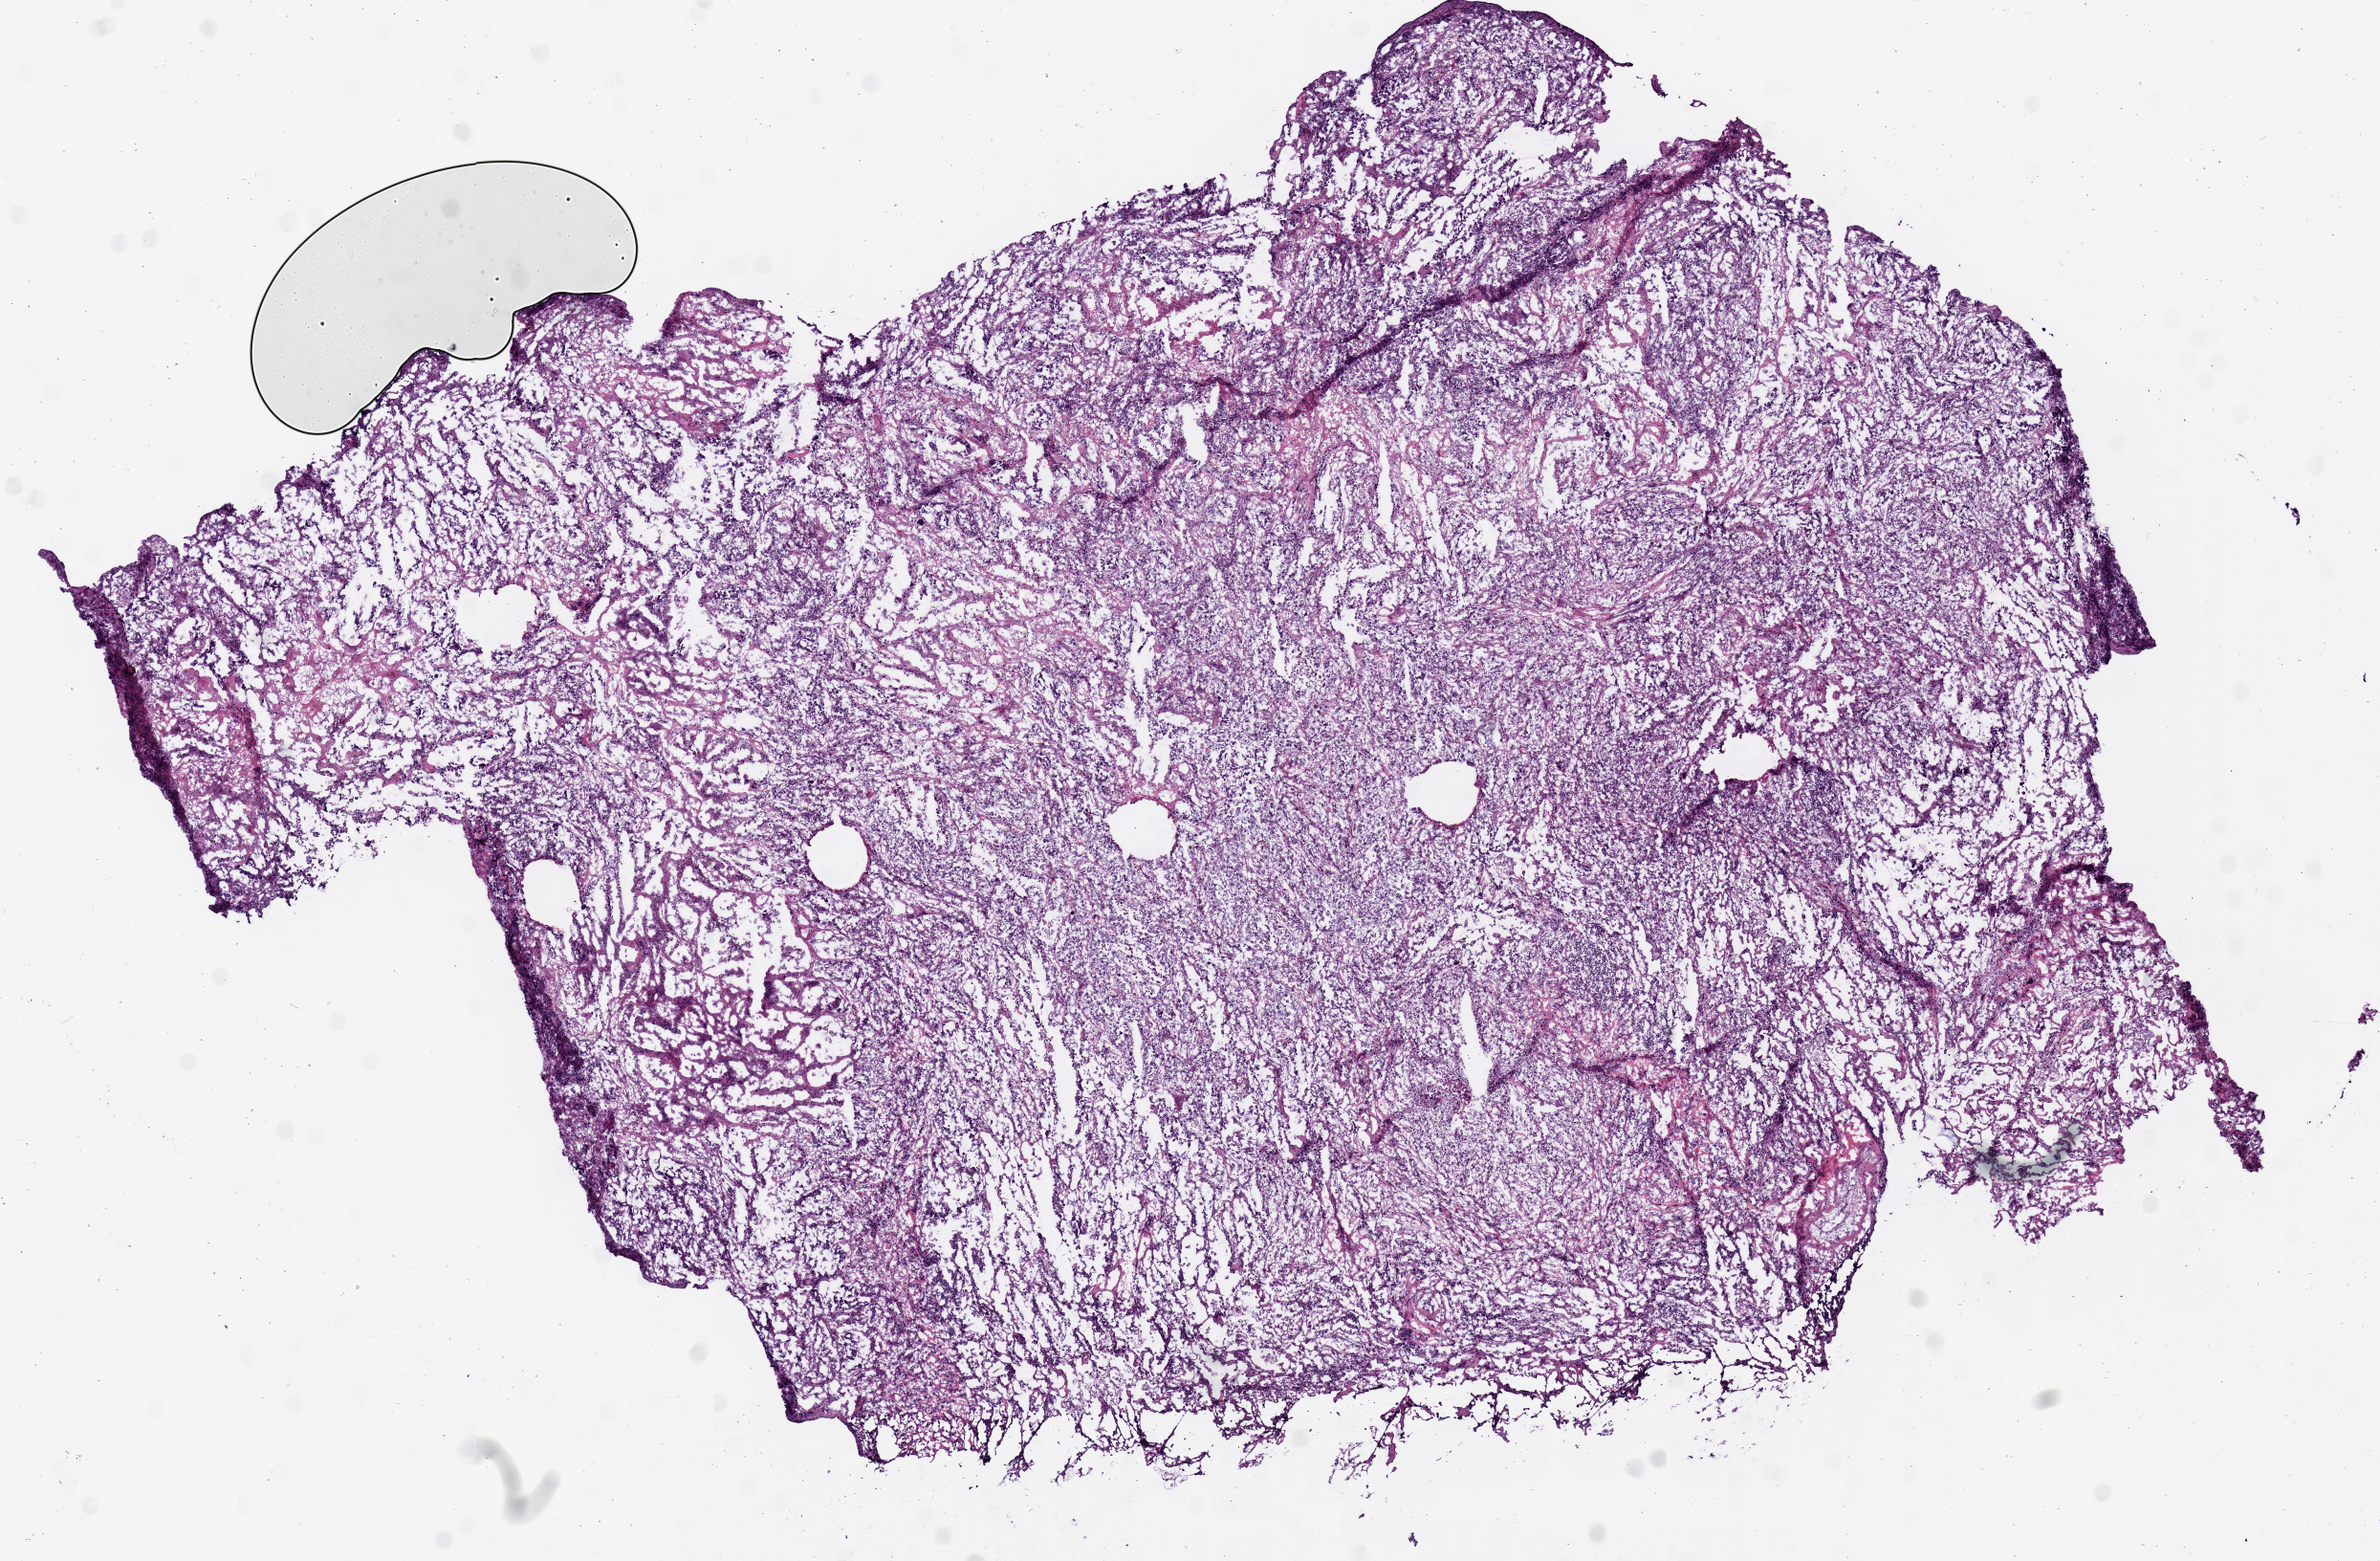
Whole-slide histology image, H&E-stained, whole scanned area (about 9.8 x 6.5 mm) shown as a low-resolution overview; frozen section; sample: primary tumour, lung. Patient: female, age at initial diagnosis 73 years.
Histologic diagnosis: Adenocarcinoma, NOS (upper lobe, lung).